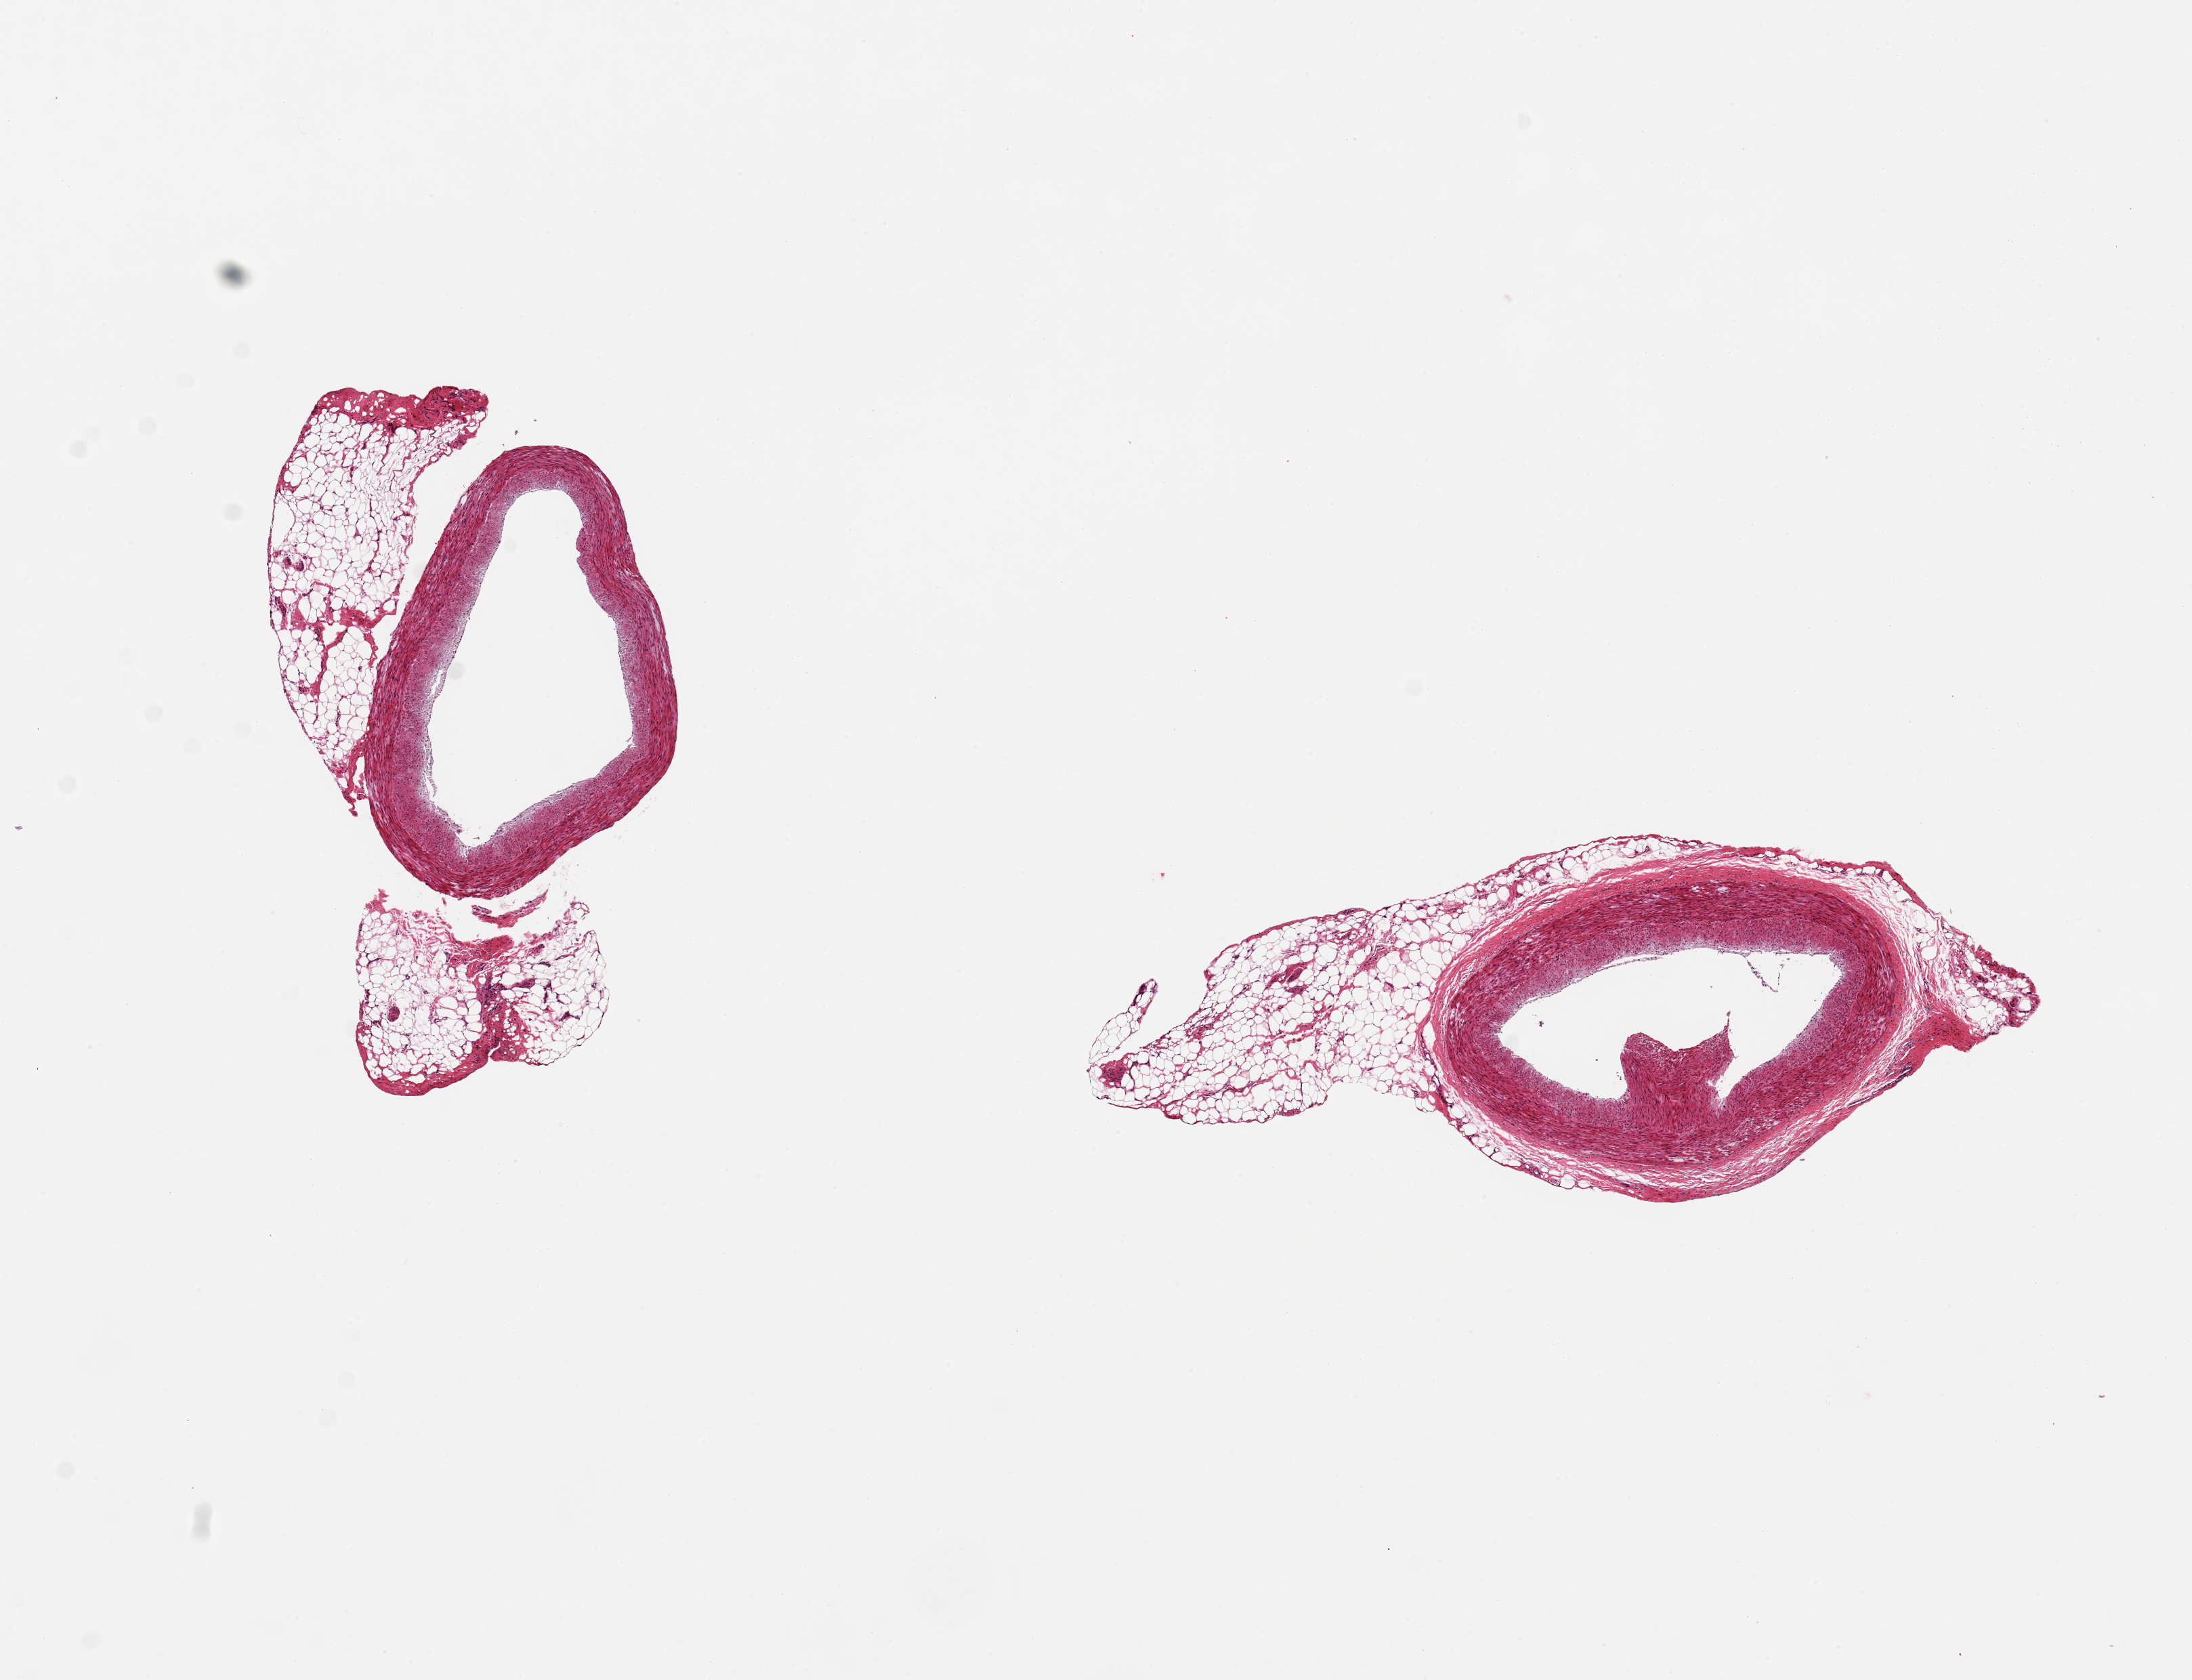
Whole-slide image, hematoxylin and eosin (H&E) stain — whole scanned area (about 12.8 x 9.8 mm) shown as a low-resolution overview; PAXgene-fixed, paraffin-embedded tissue; target tissue: coronary artery; tissue donor sample.
- pathologist's review note for this sample: 2 pieces ~2mm d. Ahdherent discontinuous fat 0.5-2mm on both